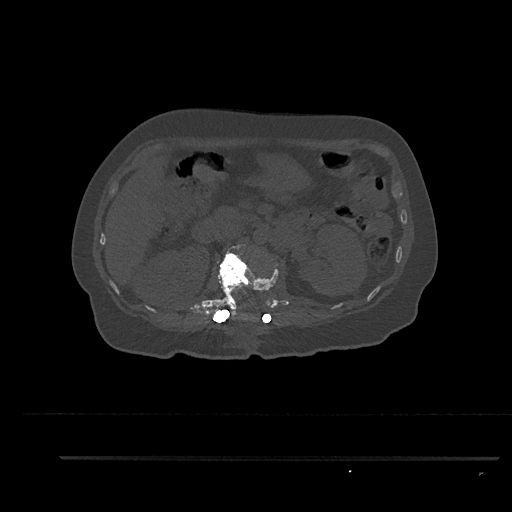
CT including the spine, one axial slice. Position 204 of 797 along the scan axis. 120 kVp. Bone window (W 1800 / L 400 HU). 512 × 512 image matrix, field of view 408 × 408 mm. Patient: female, 44 years. From the clinical record (not read from this slice): primary cancer: renal; vertebrae with lytic lesions (as recorded): L1.
Outlined on this slice (semi-automatic segmentation, software-assisted and operator-edited):
- L1 vertebra: box from (x=217, y=244) to (x=279, y=320) px